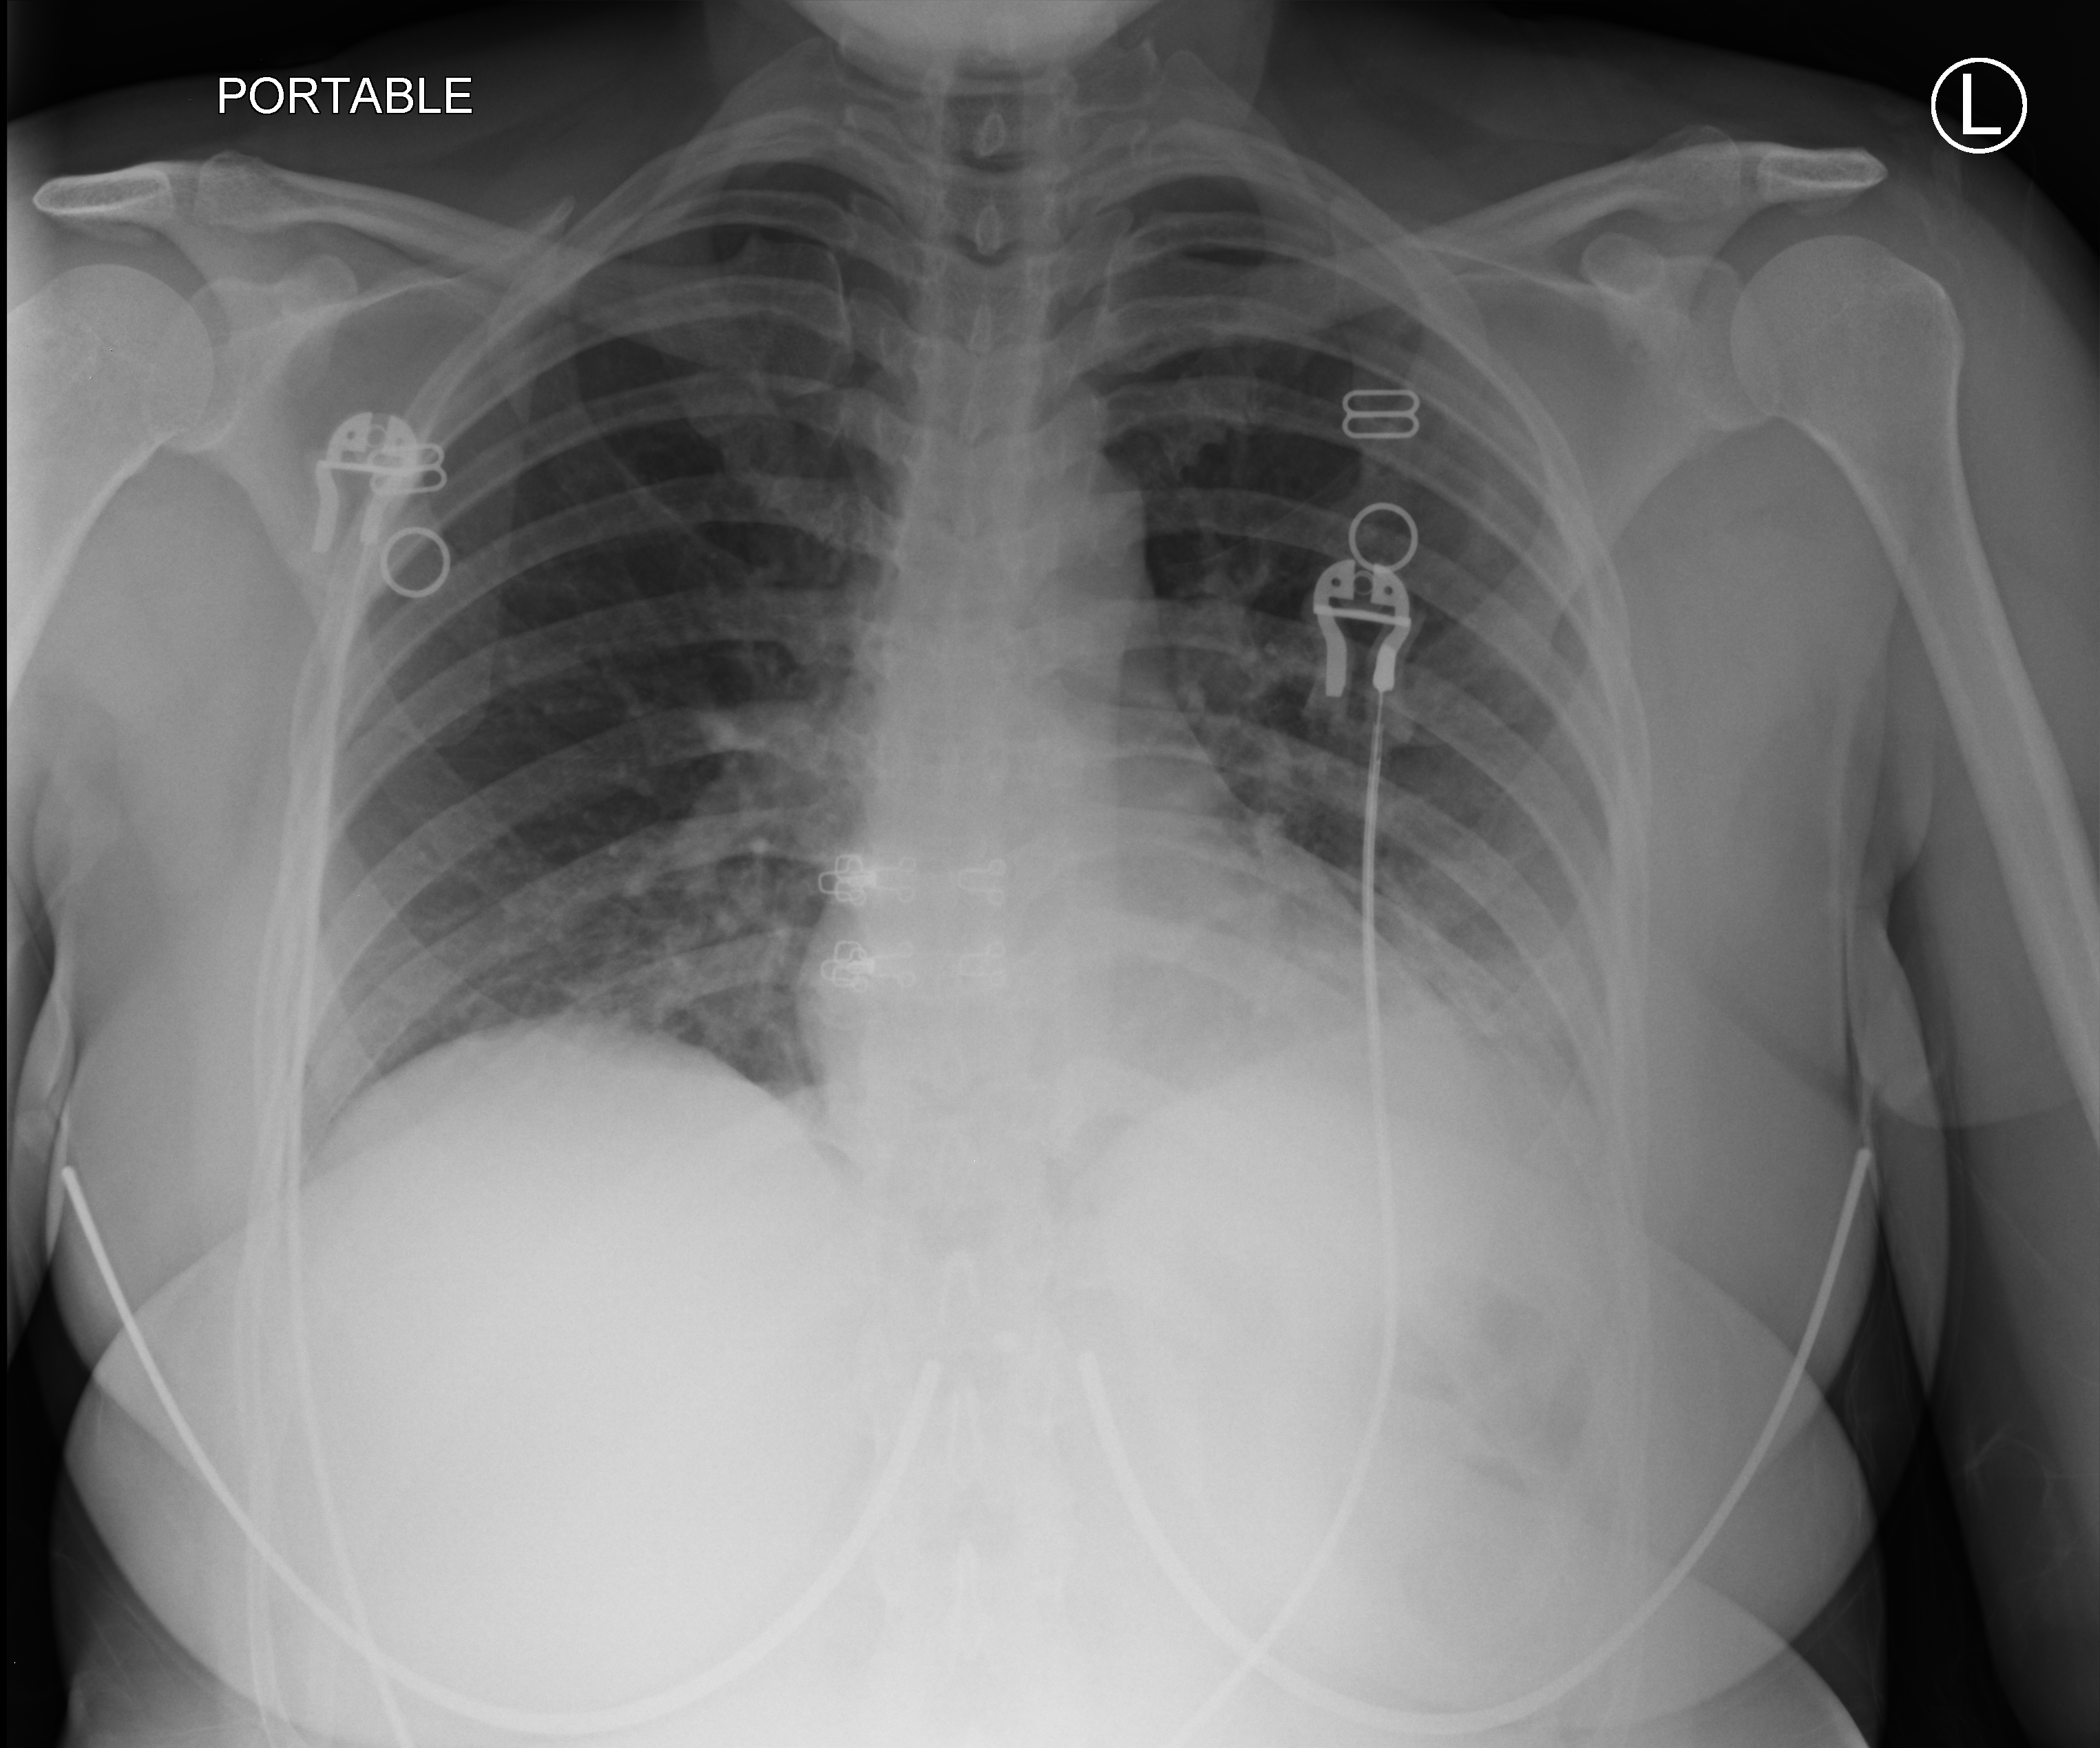
Chest X-ray (portable), anteroposterior (AP) projection. Female patient hospitalised with COVID-19, age 18–59 years.
Hospital-stay facts (about this admission, not read from this image; timing relative to this image not recorded):
- length of hospital stay: 1 day
- admitted to intensive care during this hospital stay: no